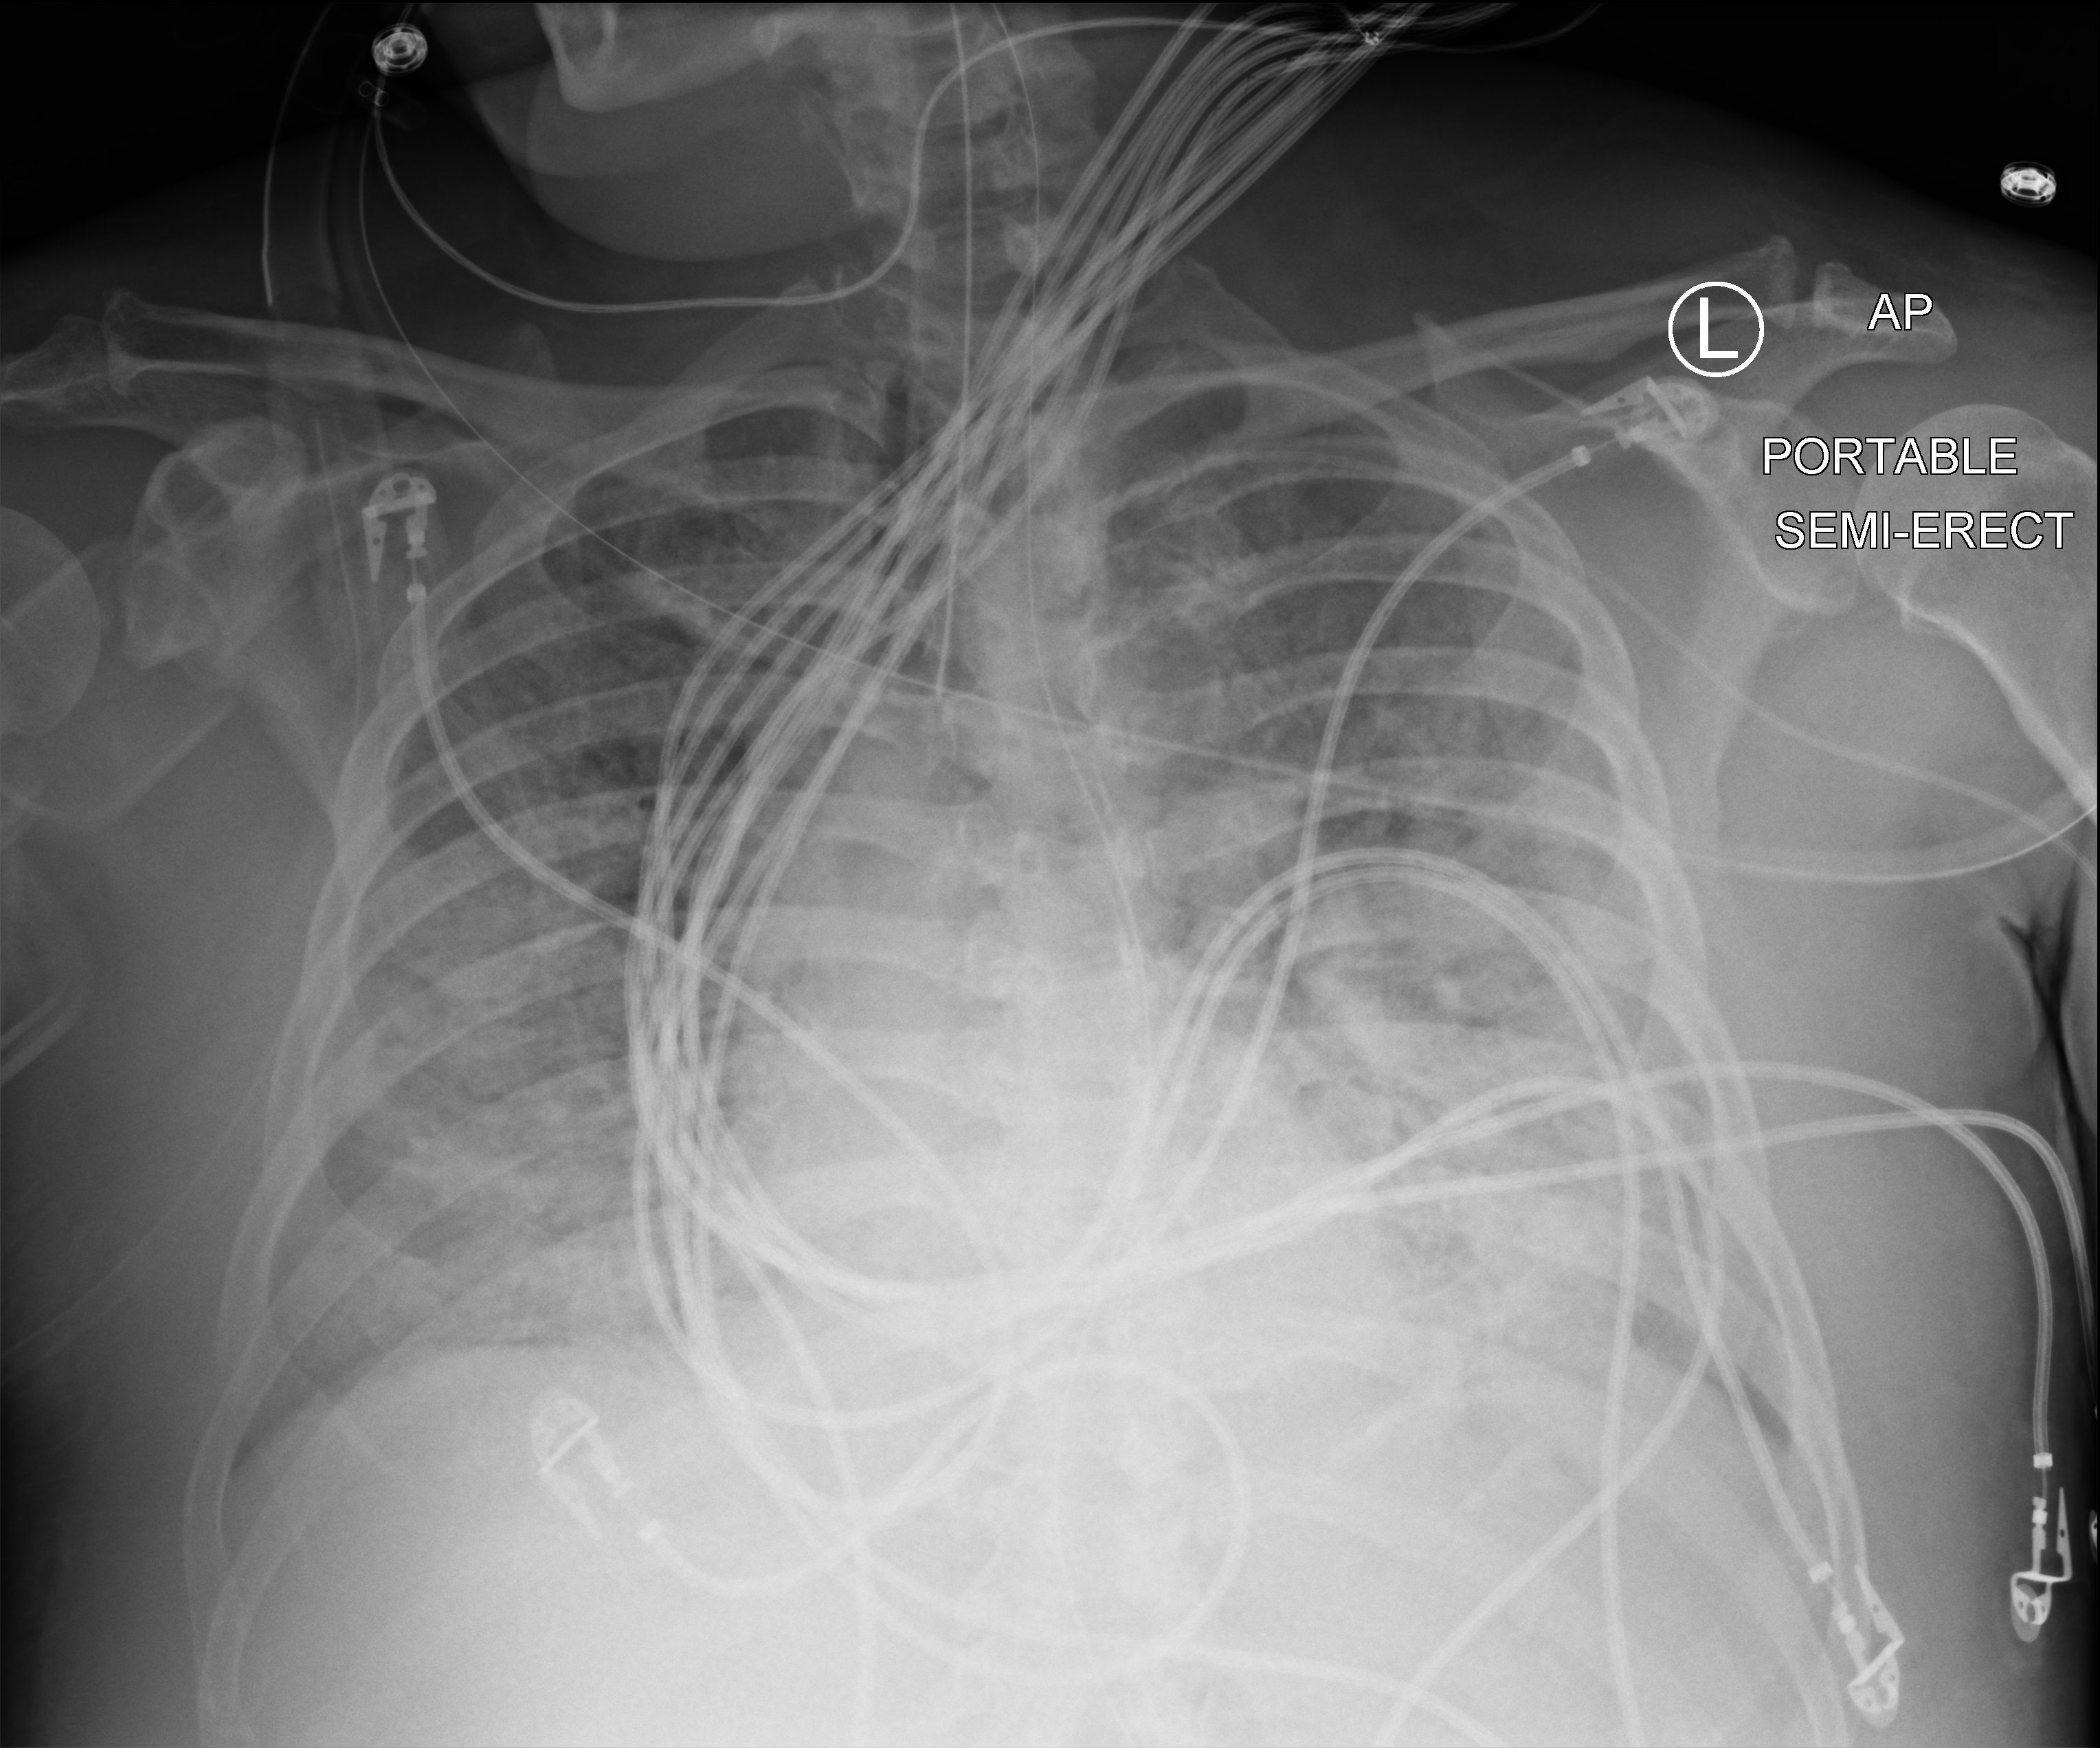
Bedside chest radiograph (computed radiography), anteroposterior (AP) projection. Patient hospitalised with COVID-19; male, aged 60–74 years.
Admission-level facts for this patient (not findings on this image; timing relative to this image not recorded):
- mechanically ventilated during this hospital stay: yes
- admitted to intensive care during this hospital stay: yes